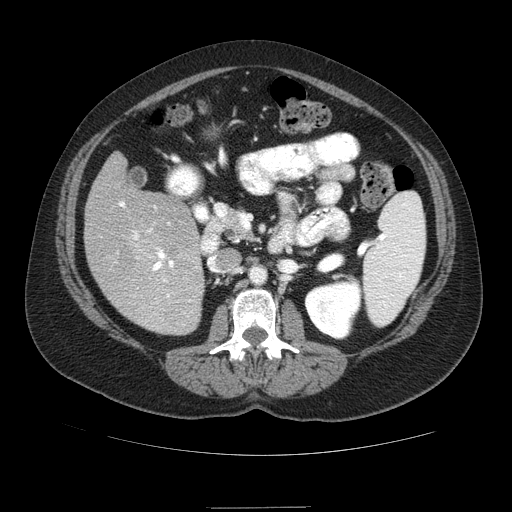
Contrast-enhanced abdominal CT (liver protocol), one axial slice. Slice 35 of 89 in the series (ordered by position). 120 kVp. Soft-tissue window (W 400 / L 40 HU). 2.5 mm slice thickness. 512 × 512 image matrix, field of view 400 × 400 mm. From the clinical record (not read from this slice): diagnosis: hepatocellular carcinoma (patient treated with transarterial chemoembolisation; whether this scan precedes or follows treatment is not stated here); TNM stage (as recorded): Stage-IIIB; Child-Pugh class: A; tumour nodularity: multinodular.
Outlined on this slice (semi-automatically segmented with operator editing):
- liver parenchyma outside the tumour (the mass and vessels are separate outlines, so this box may not span the whole liver): bounding box (x1, y1, x2, y2) in pixels: (84, 153, 204, 334)
- liver vessels: (119, 201, 191, 301)